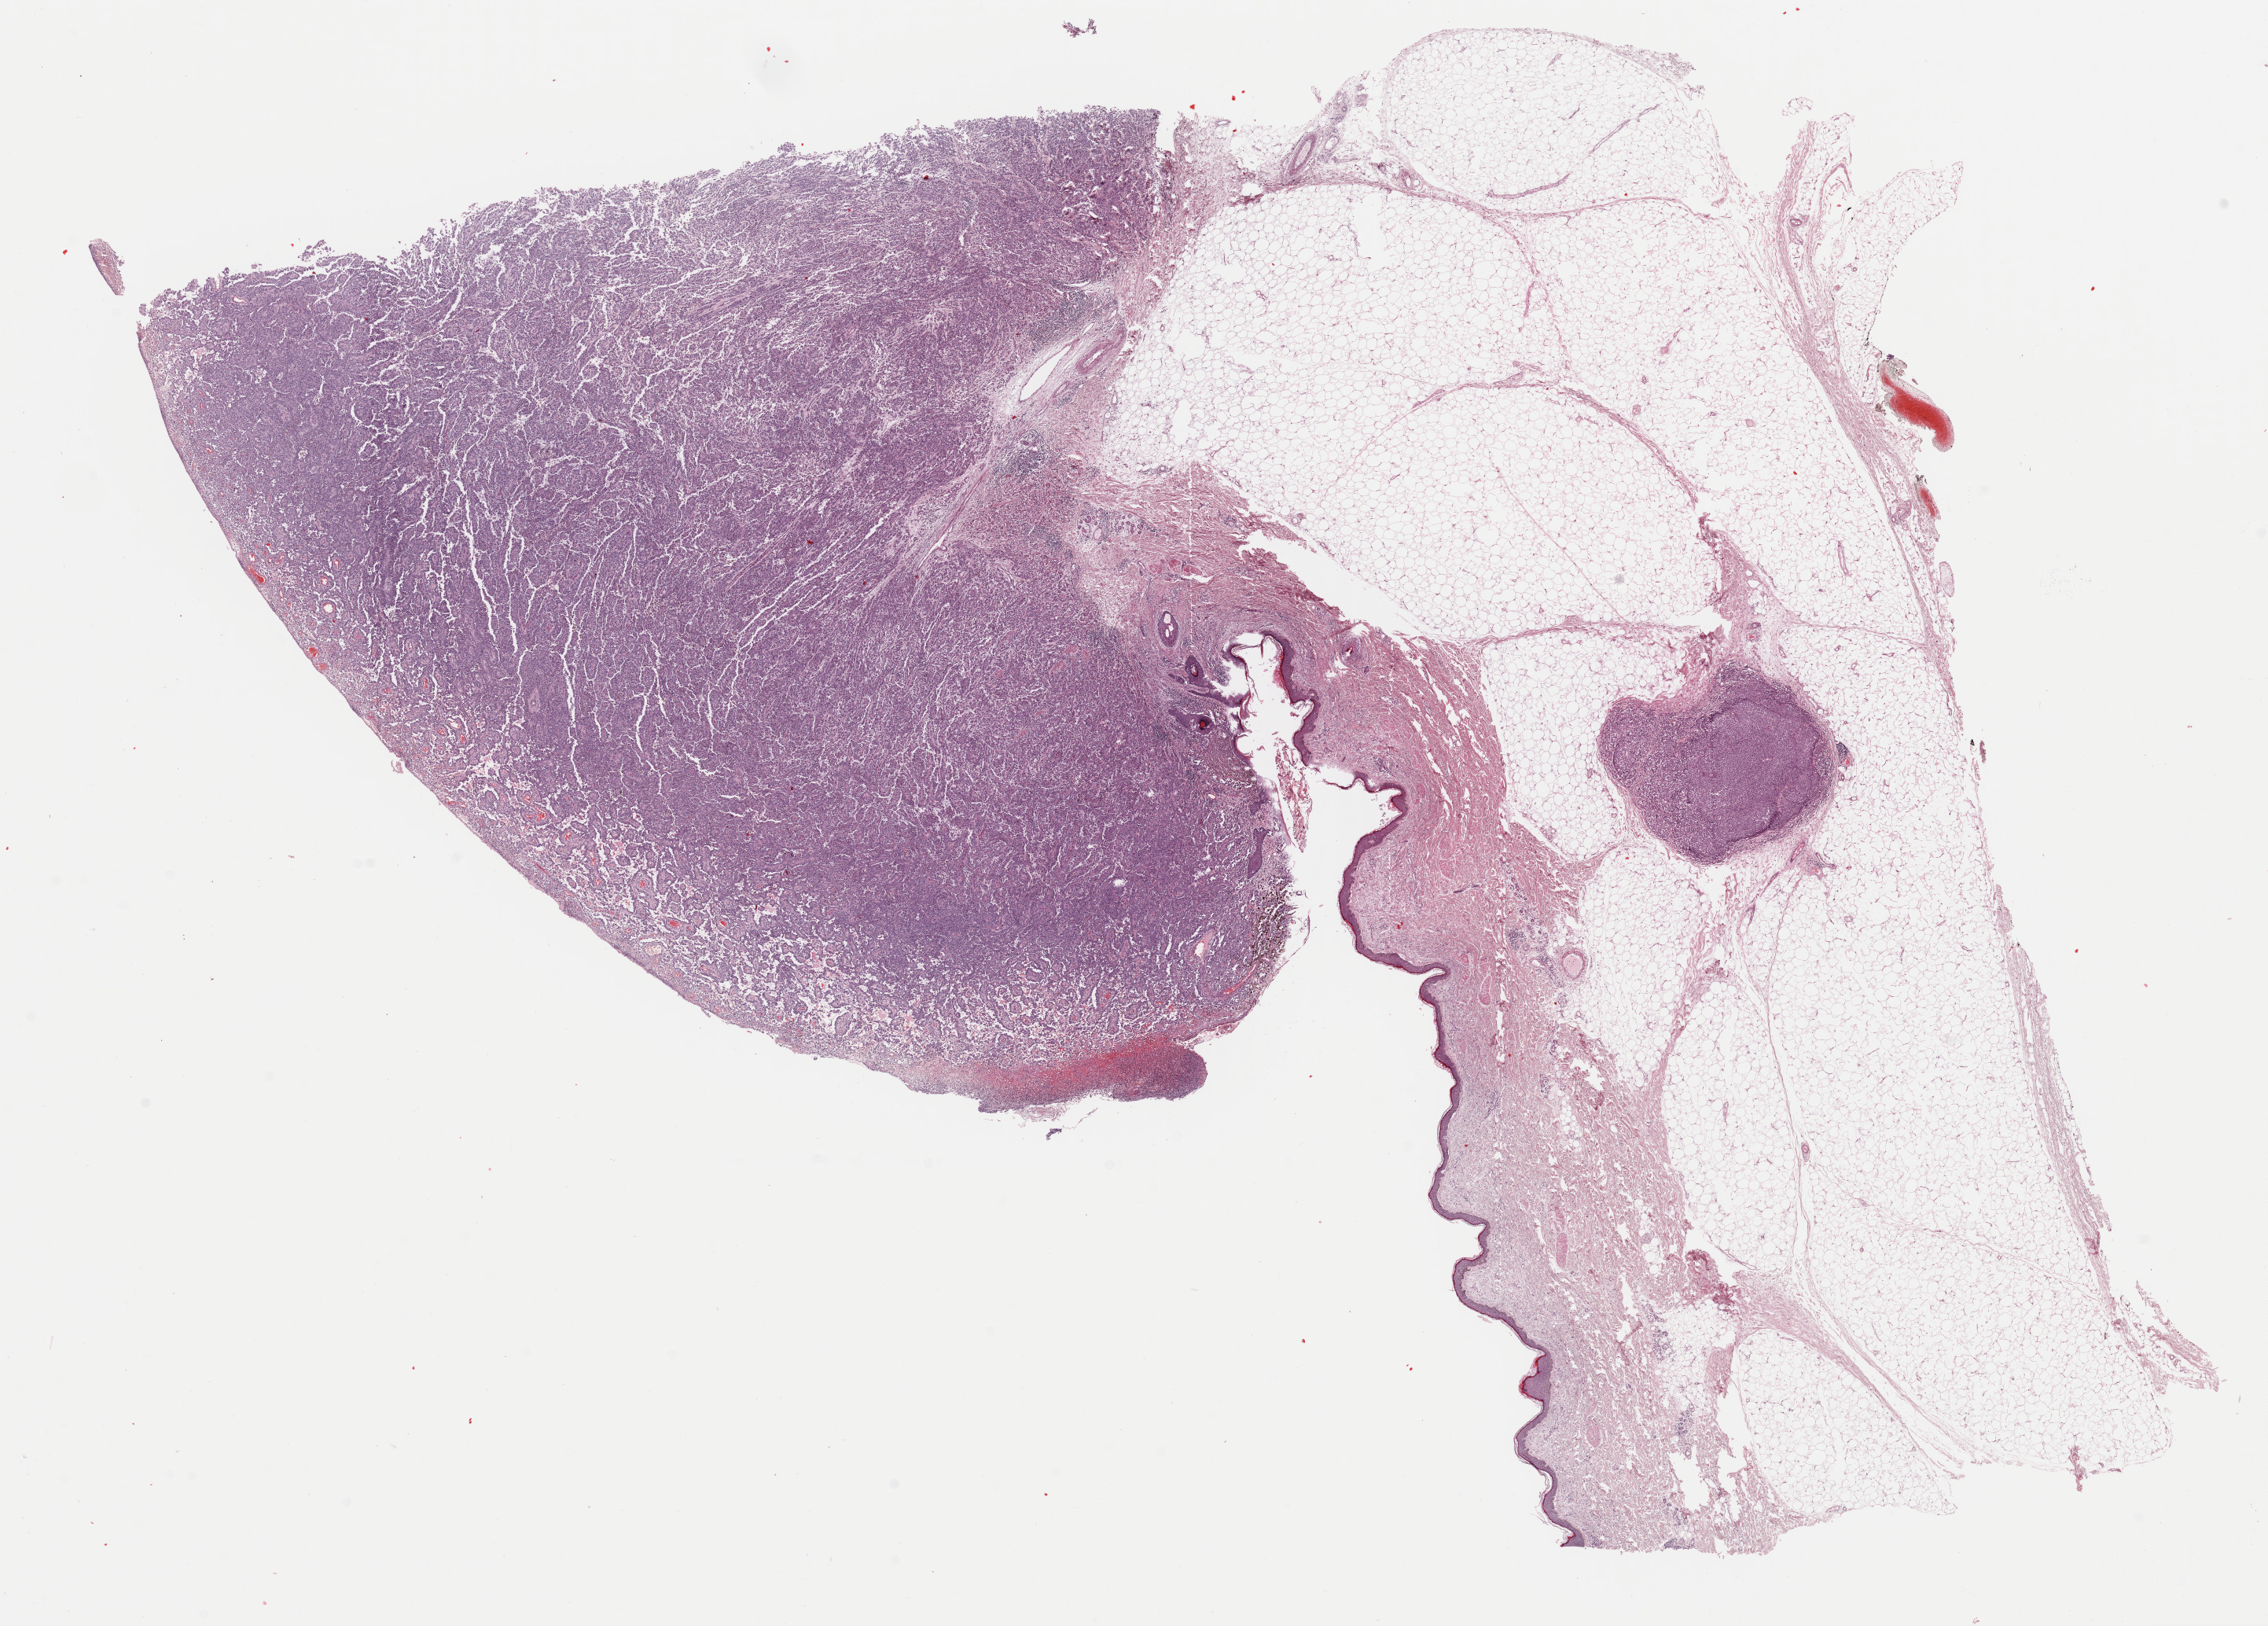
Digitized H&E tissue section (whole slide), whole scanned area (about 22.8 x 16.3 mm) shown as a low-resolution overview; FFPE section; primary tumour sample from the skin. Male patient; age at initial diagnosis 54 years.
TNM: T4b N3 M0. AJCC pathologic stage: IIIC. Pathologic diagnosis: Malignant melanoma, NOS.